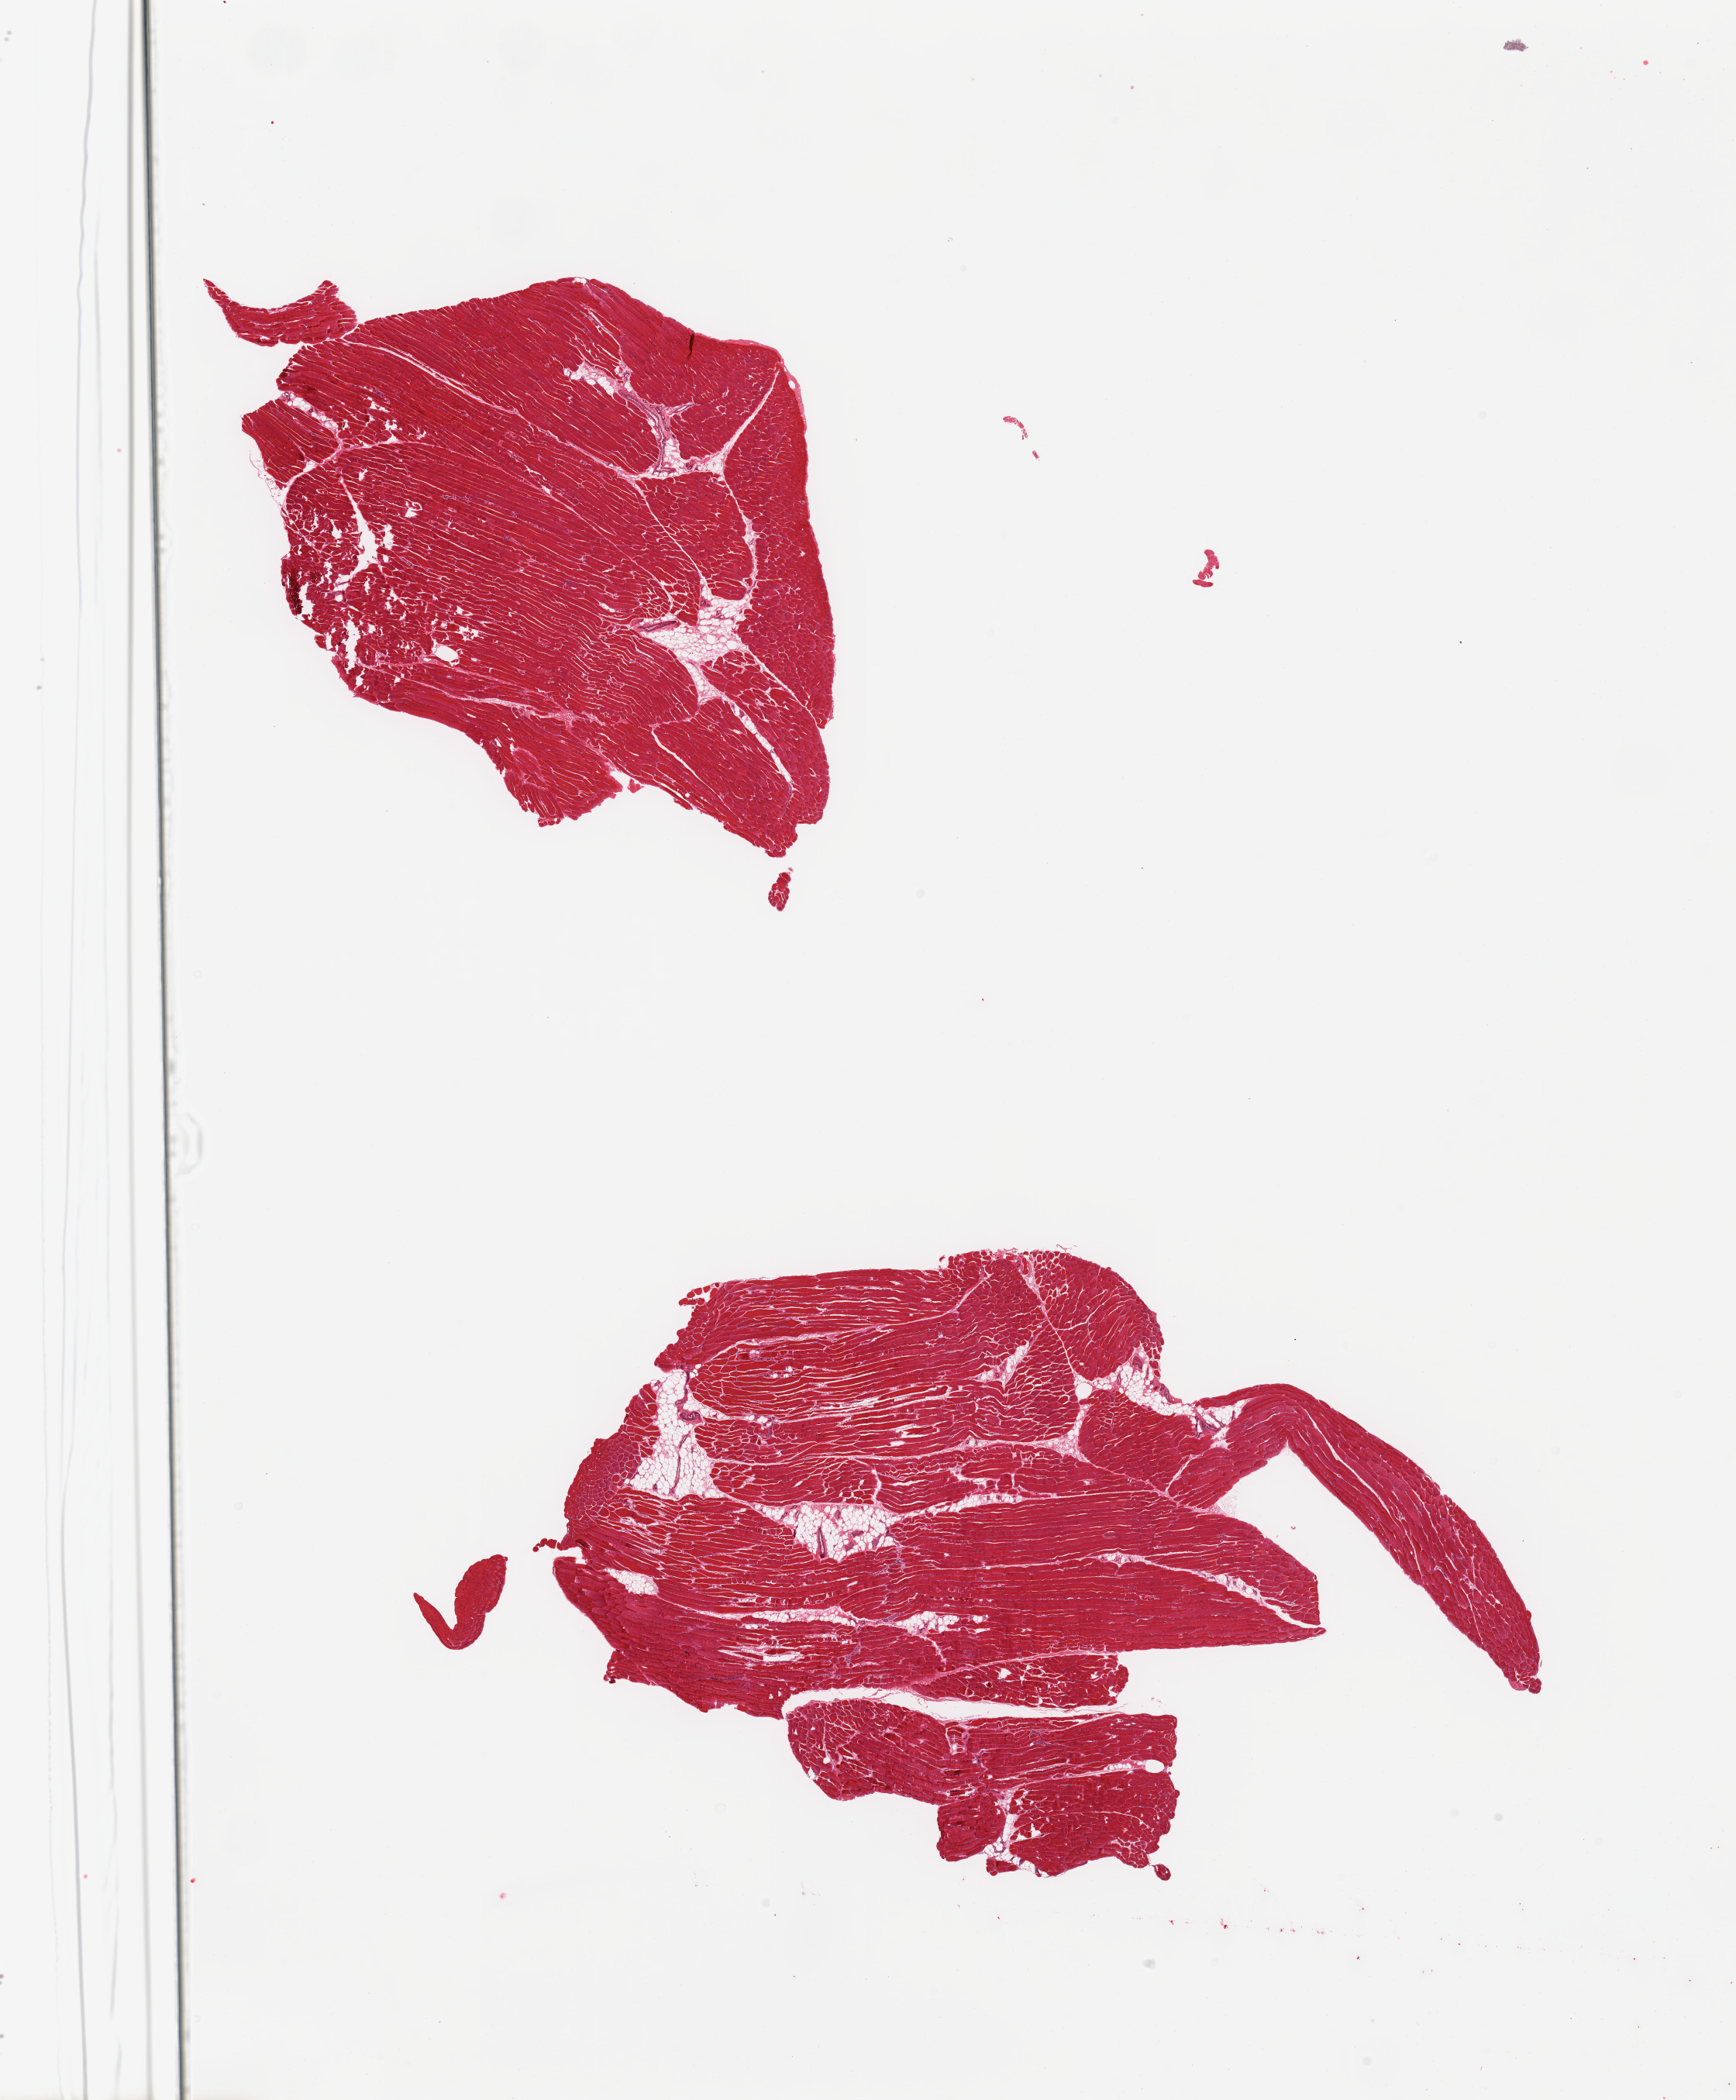
Digitized hematoxylin and eosin (H&E)-stained section, brightfield, low-resolution overview of the scanned area, about 17.7 x 21.4 mm (slide scanned at 20x). PAXgene-fixed, paraffin-embedded tissue. Sampled site (target tissue): skeletal muscle. Donor tissue sample. Male donor.
Pathologist's review note for this sample: 2 pieces; internal fat <5%.